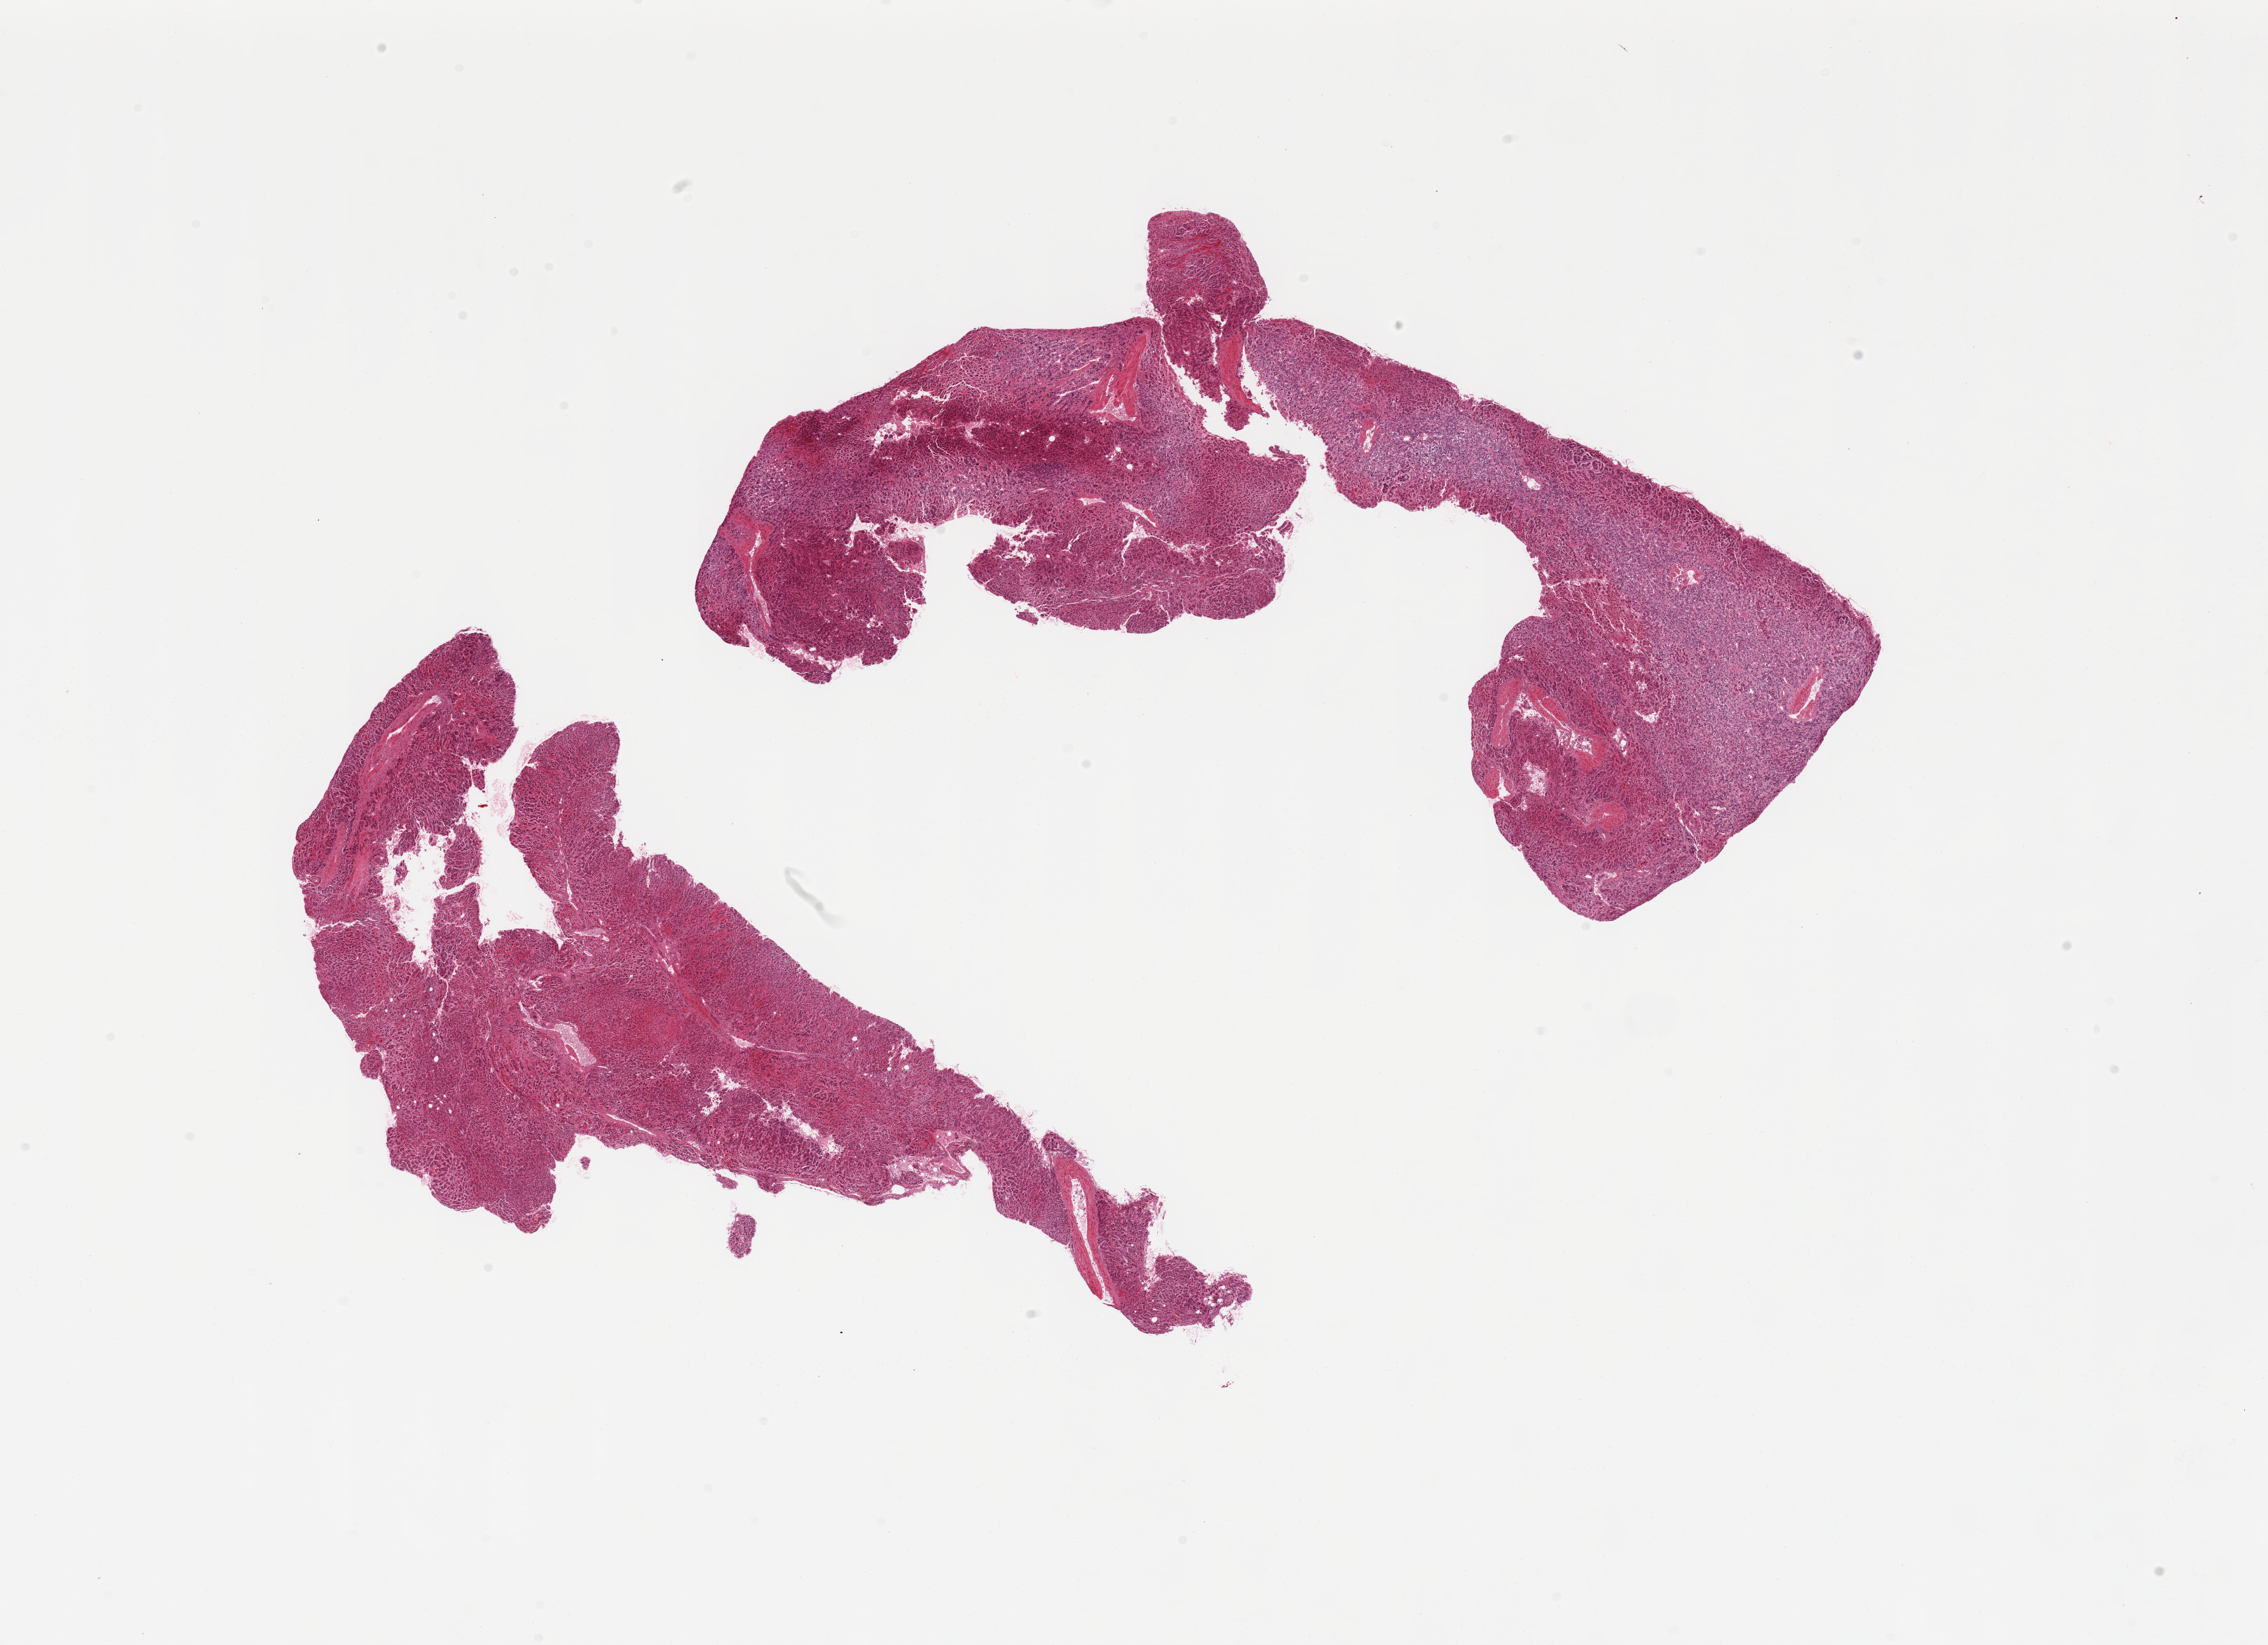
Hematoxylin and eosin (H&E) whole-slide image, whole scanned area (about 25.6 x 18.6 mm, acquisition: 20x scan) shown as a low-resolution overview. PAXgene-fixed paraffin-embedded (PFPE) section. Sampled site (target tissue): adrenal gland. Tissue donor sample.
* reviewer comment on this tissue sample: 2 pieces; well trimmed non-fatty